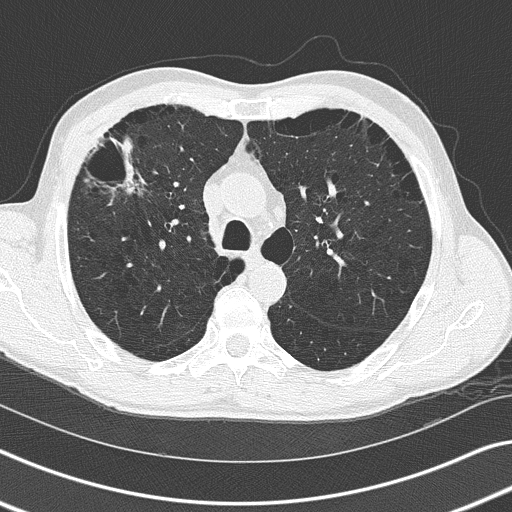
Low-dose screening chest CT, axial slice. Third screening round (two years after baseline). Lung window (W 1500 / L -600 HU). 2 mm slice thickness. 120 kVp. 512 × 512 image matrix, field of view 340 × 340 mm. Male, age 66 years at enrolment. Current smoker at enrolment.
Expert-annotated lung lesion, bounding box <84,121,160,208> (left, top, right, bottom; pixels). Screening reader's record for this exam (one nodule recorded; not confirmed to be the boxed lesion): non-calcified nodule or mass ≥4 mm, left lower lobe, 9 × 8 mm, smooth margins, soft tissue attenuation, pre-existing on the prior screen: yes; interval growth: no. Note: the box lies in the patient's right hemithorax on this image, whereas the reader's record names the left lung; they may be different findings. Lung cancer was diagnosed 285 days after this screen: squamous cell carcinoma, adenoid, right upper lobe, poorly differentiated (G3), stage IIB (AJCC 6th edition), 50 mm at pathology.